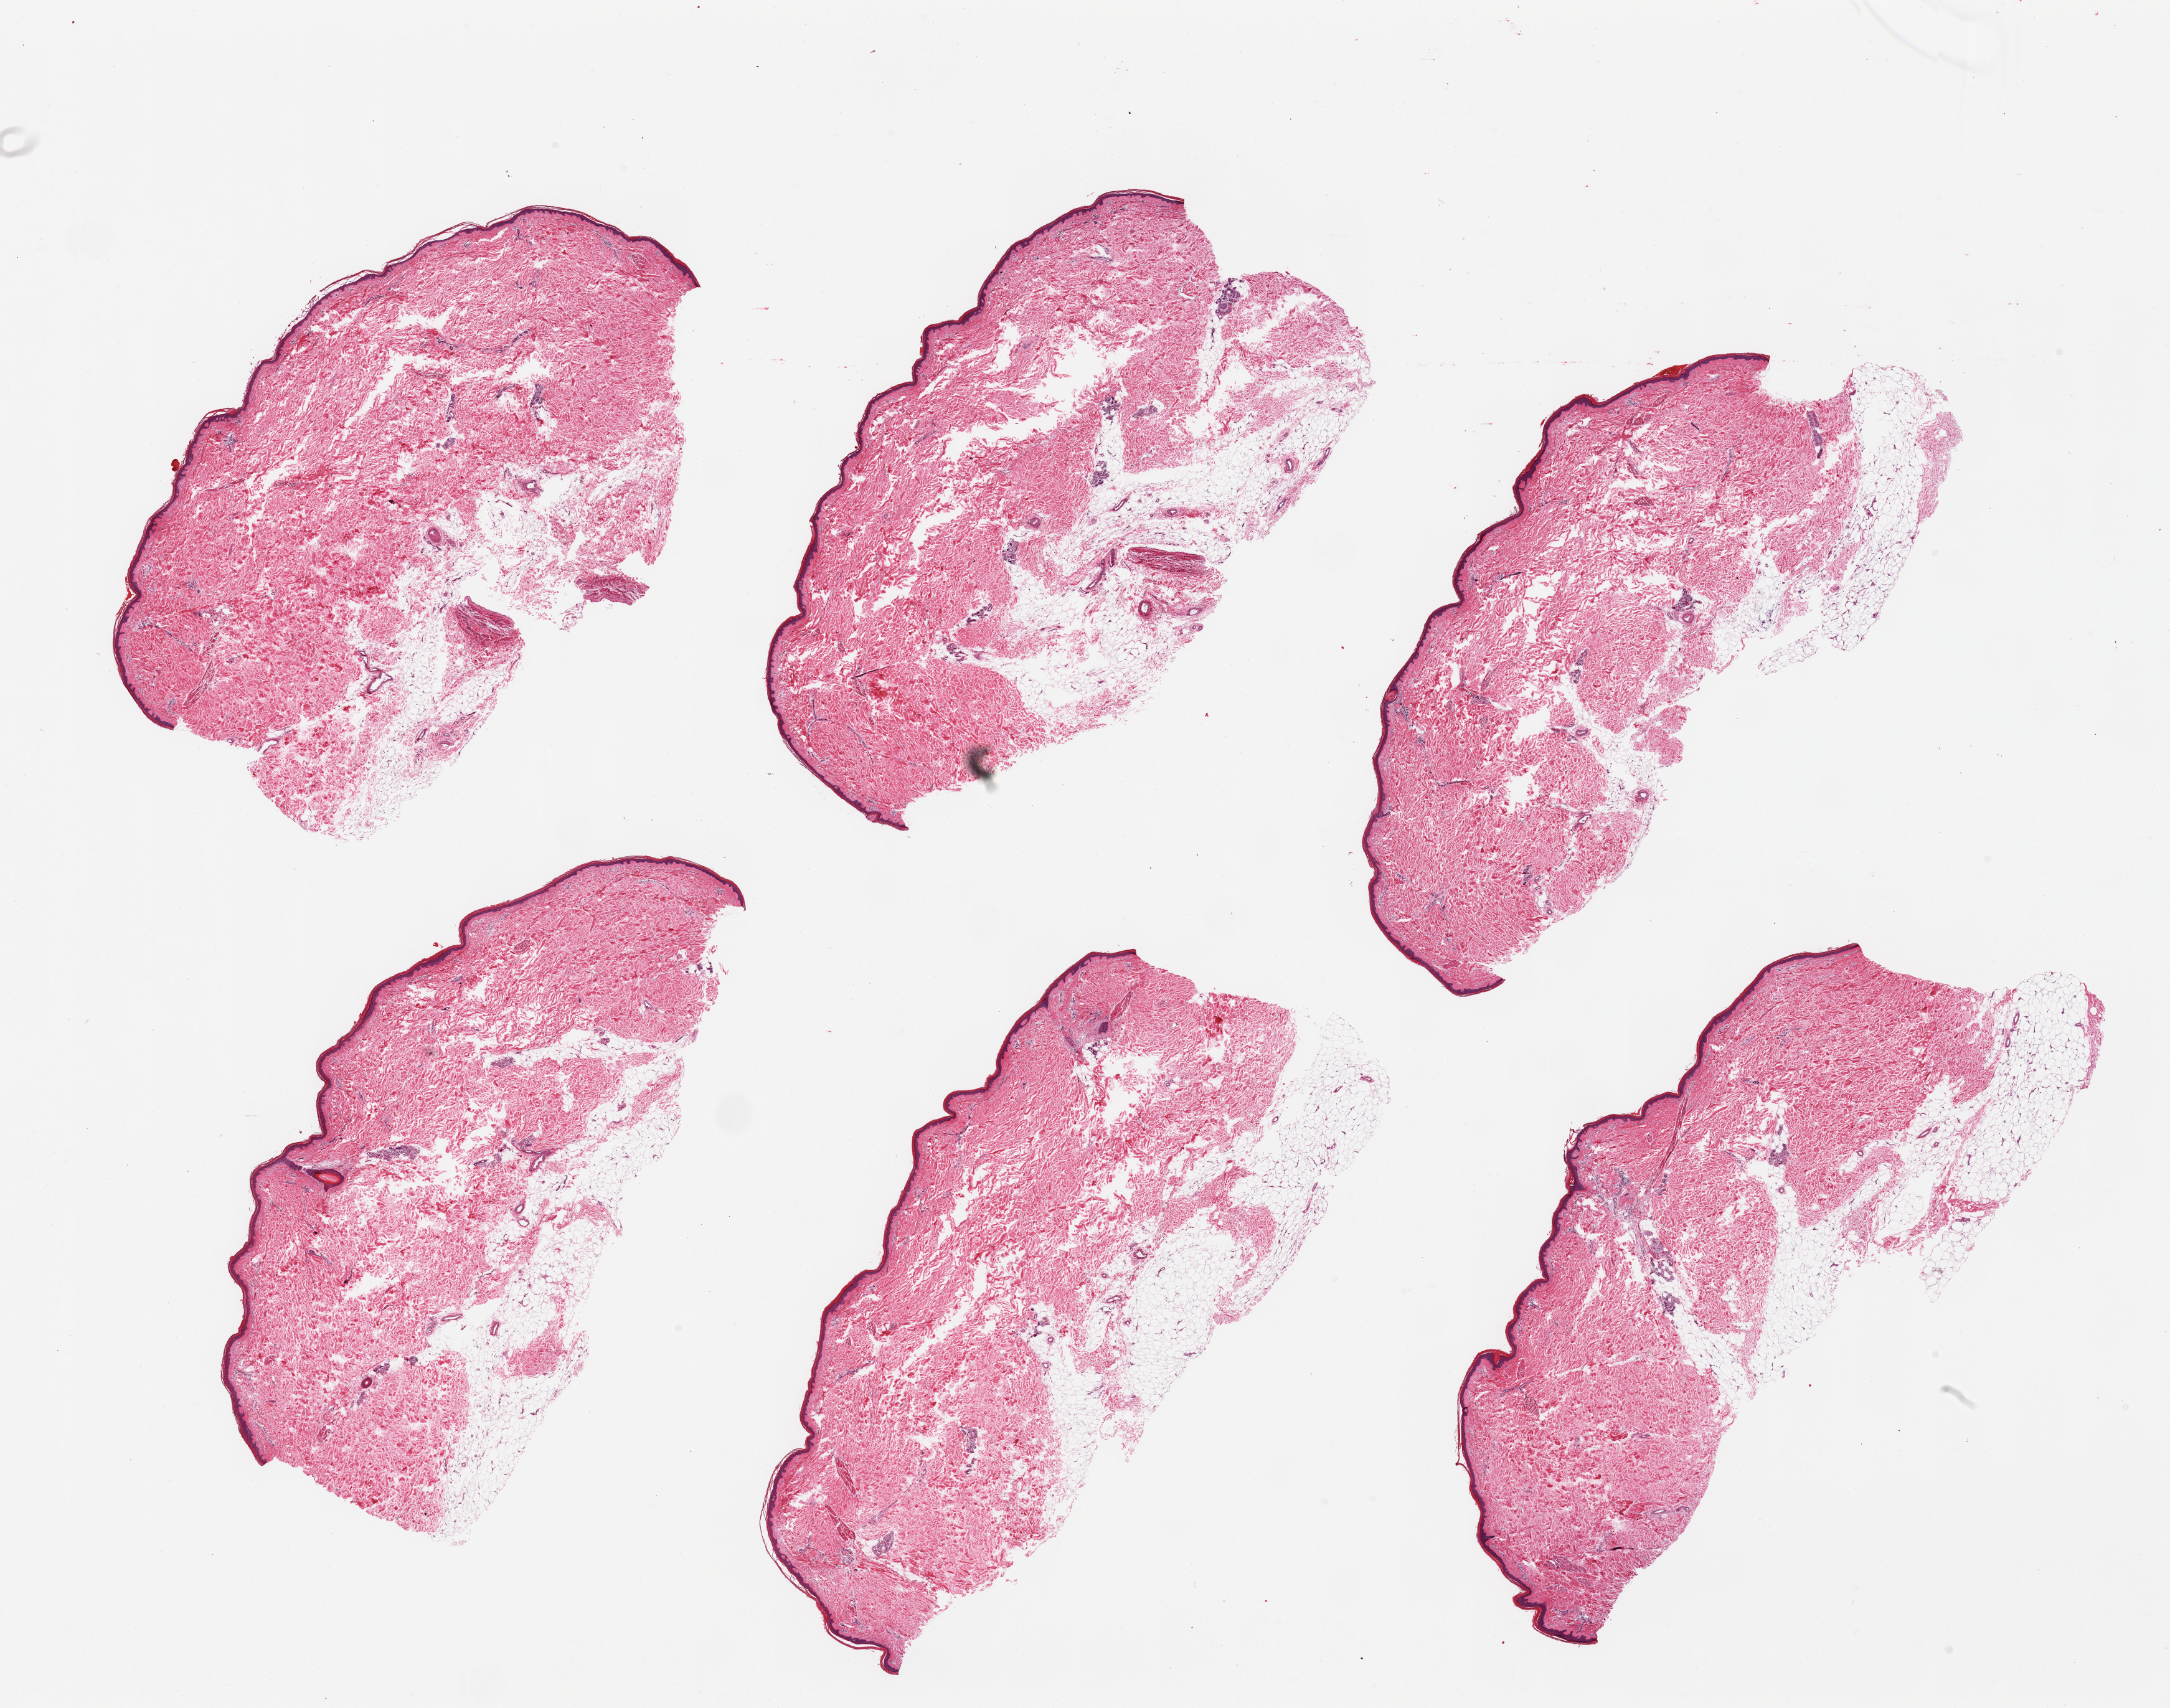
Digitized hematoxylin and eosin (H&E)-stained section, brightfield, low-resolution overview of the scanned area, about 27.6 x 21.7 mm, PAXgene-fixed paraffin-embedded (PFPE) section, sampled site (target tissue): skin of lower leg, donor tissue sample. Donor sex: female.
Reviewer comment on this tissue sample: 6 pieces; 20-40% dermal fat; partly fragmented.